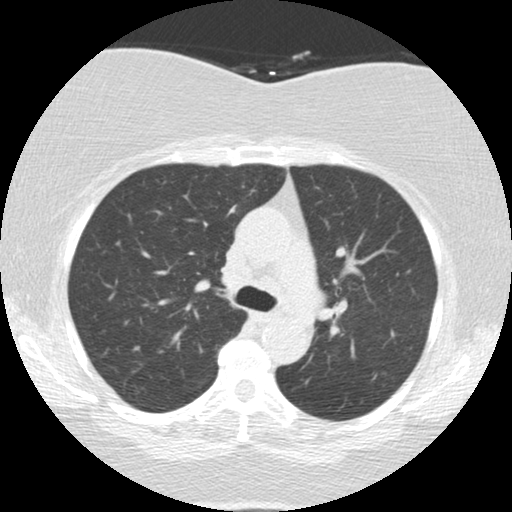
Low-dose screening chest CT, one axial slice; position 90 of 136 along the scan axis; reconstruction kernel STANDARD; lung window (W 1500 / L -600 HU); 512 × 512 image matrix.
Annotated regions visible in this slice (outlined manually by an expert reader):
- lesion 2 (tumor, mediastinum): bounding box [x1, y1, x2, y2] px = [307, 289, 328, 313]